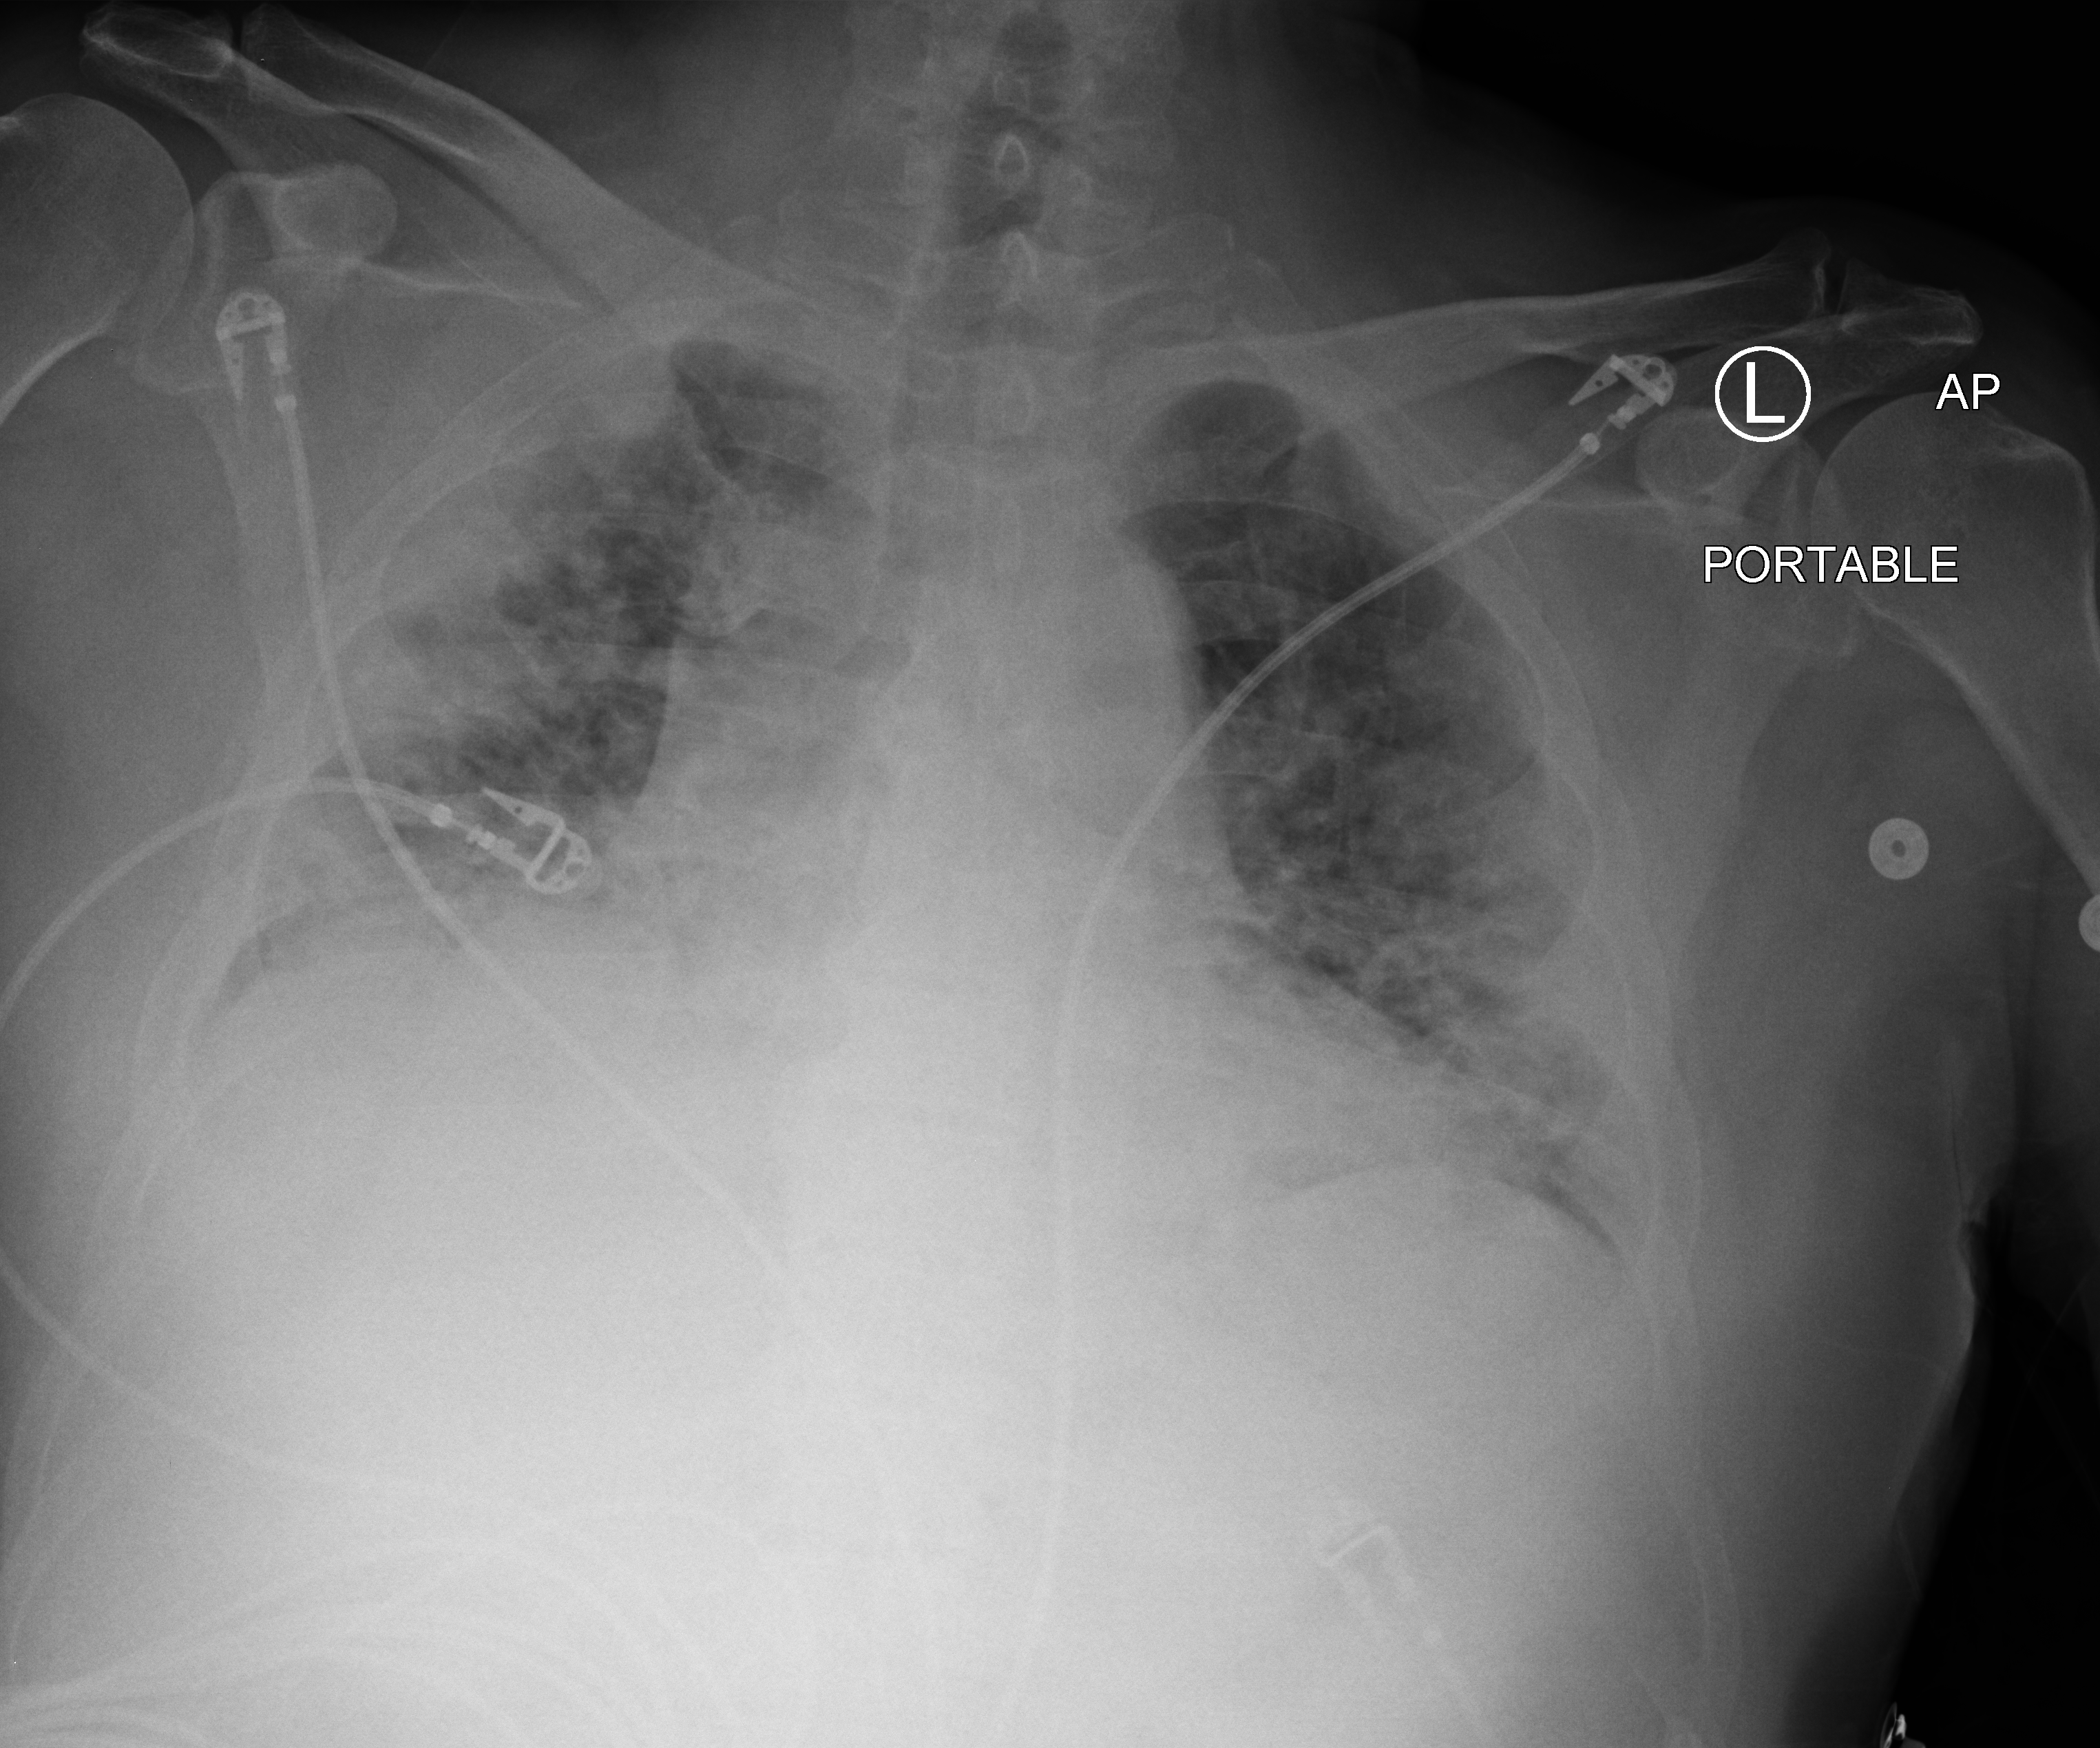
Chest X-ray (portable); anteroposterior (AP) projection. Male patient hospitalised with COVID-19, age 60–74 years.
From the hospital-stay record, not from the radiograph (when in the stay this image was taken is not recorded): mechanically ventilated during this hospital stay: no; admitted to intensive care during this hospital stay: no.